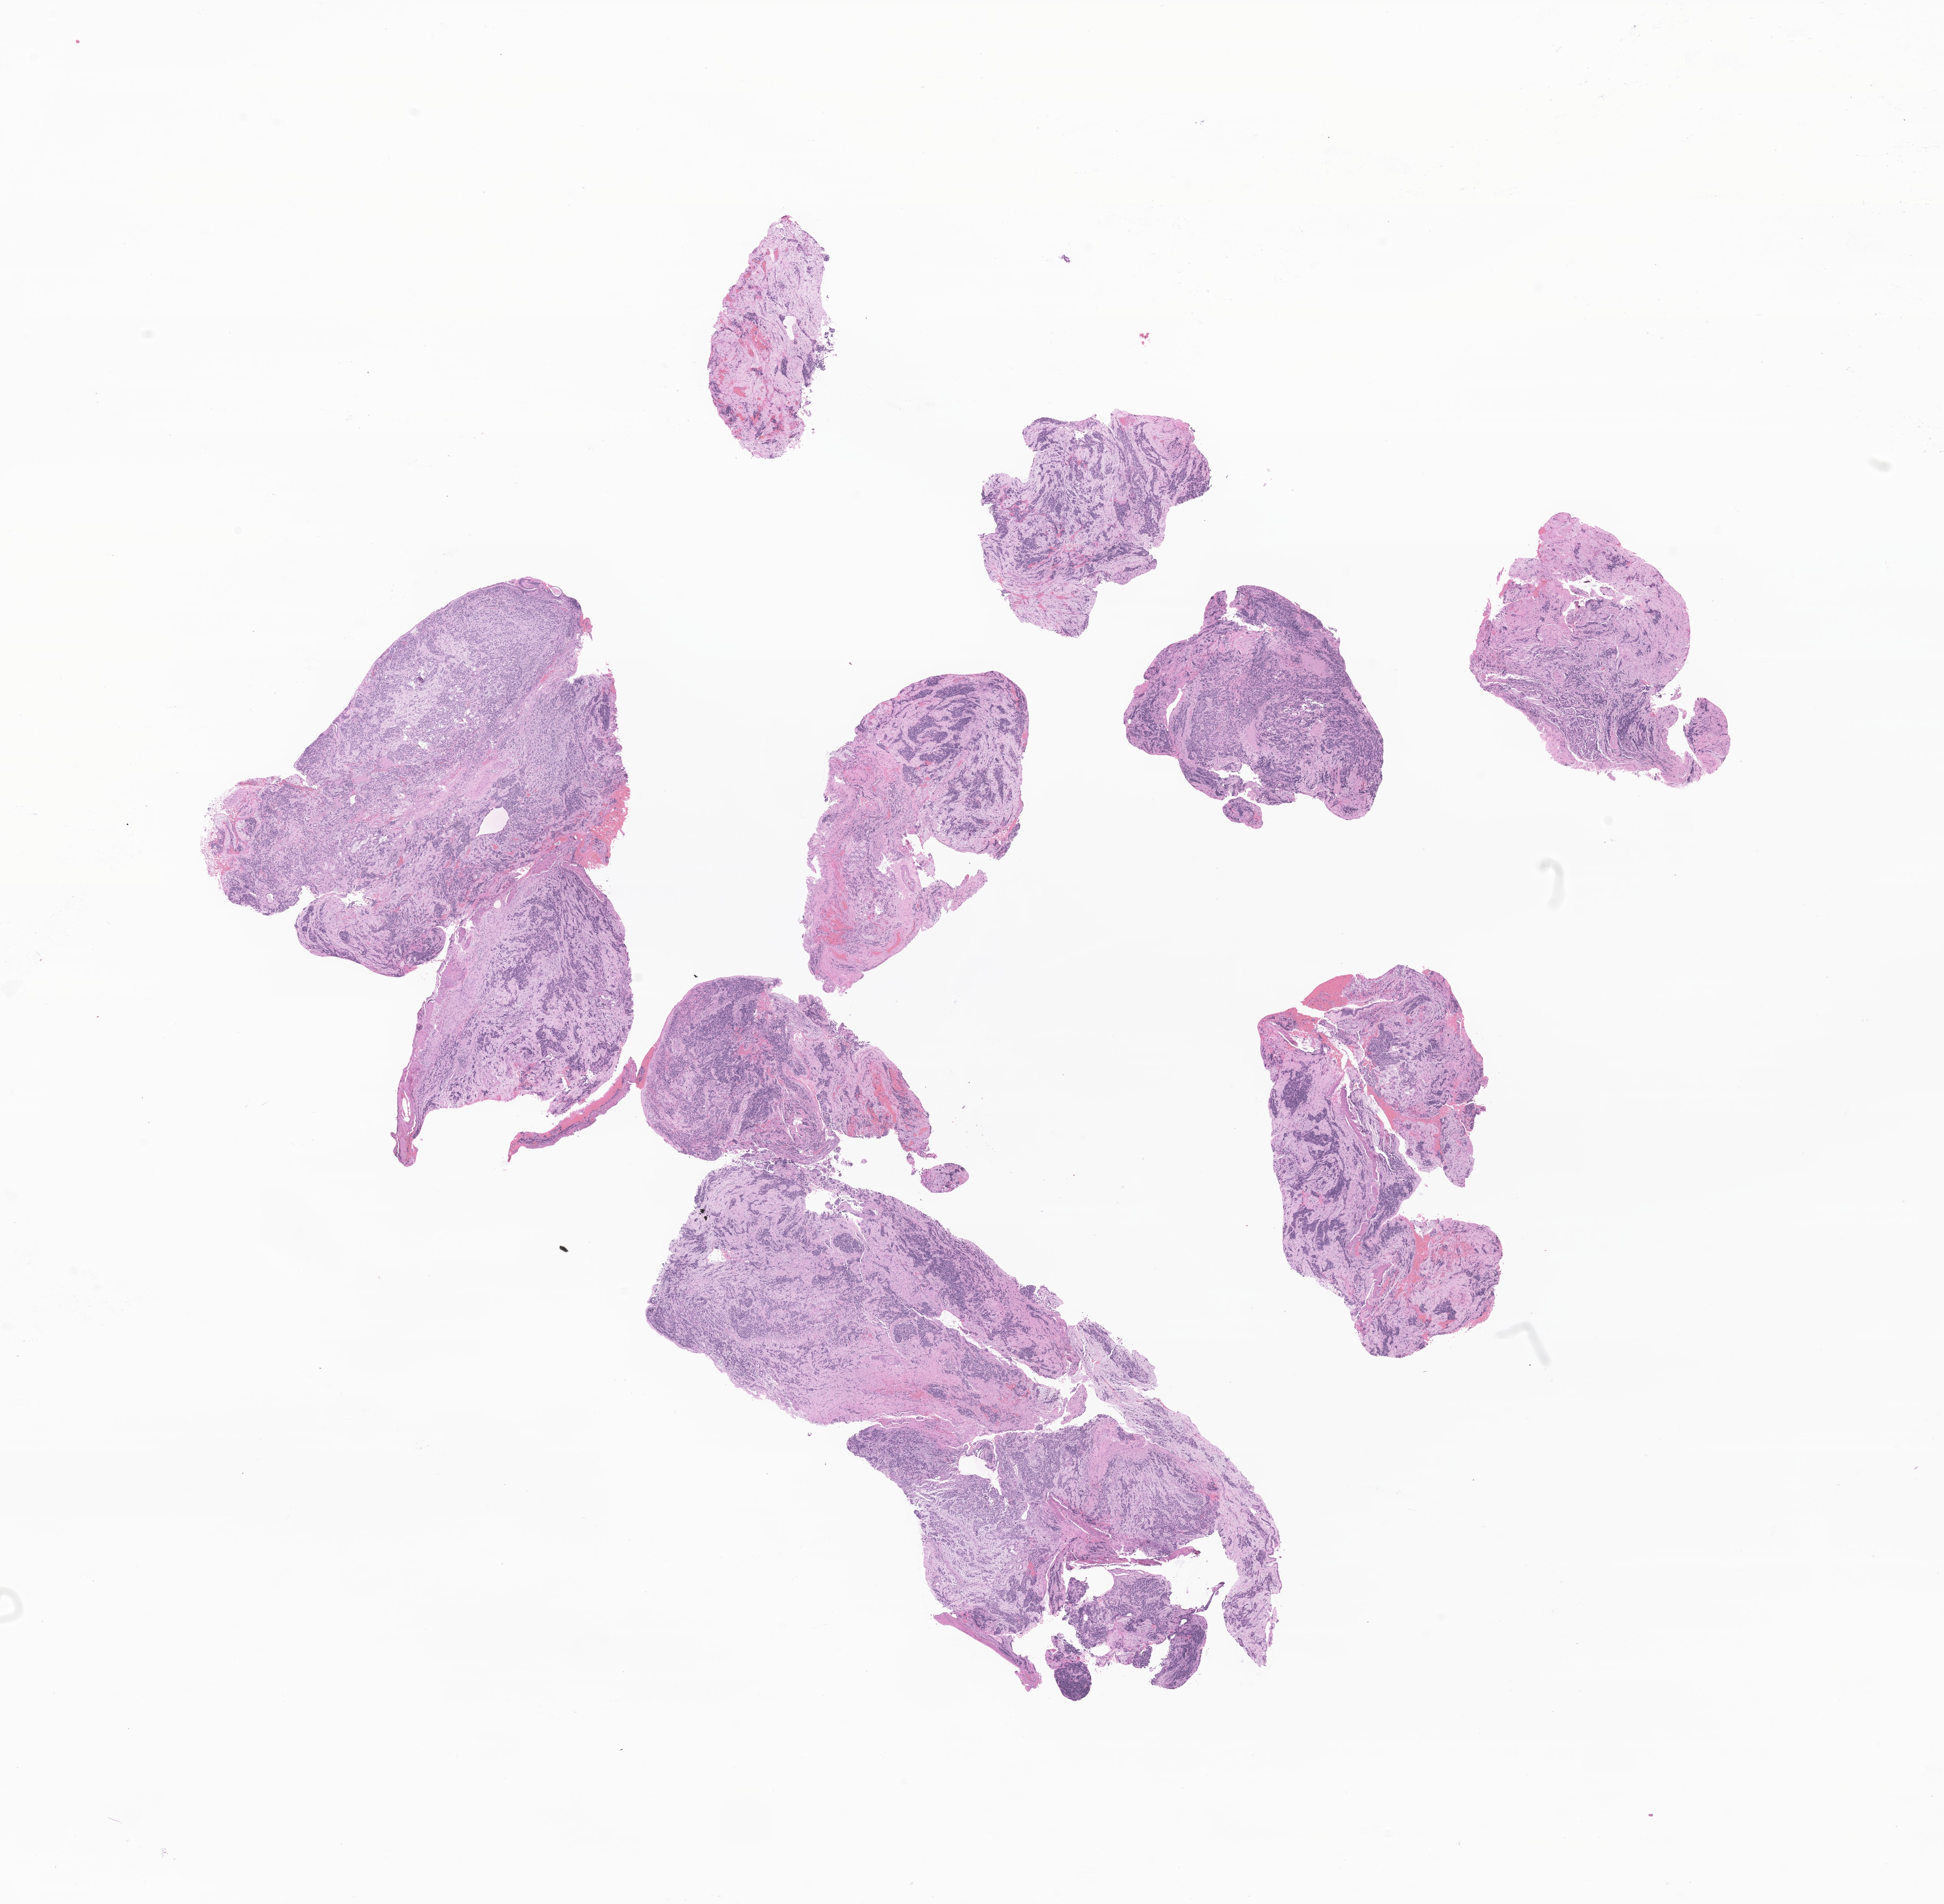
Digitized hematoxylin and eosin (H&E)-stained section of tumor tissue from the ethmoid sinus, whole scanned area (about 18.3 x 17.9 mm) shown as a low-resolution overview. FFPE section. Male patient, age 181 months (15 years 1 month).
Recorded diagnosis: Alveolar rhabdomyosarcoma.